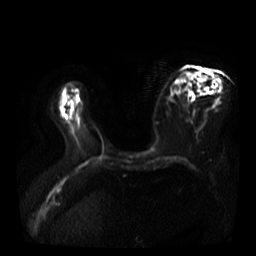
Breast MRI, one axial slice; position 19 of 40 along the scan axis; diffusion-weighted series; image 2 of 4 stored at this slice position (different b-values; order by instance number); 3 T; 5 mm slice thickness; 256 × 256 image matrix, field of view 360 × 360 mm. Female patient.
Structures marked on this image (expert manual segmentation):
- tumour on diffusion-weighted imaging: bounding box [x1, y1, x2, y2] px = [216, 79, 219, 83]